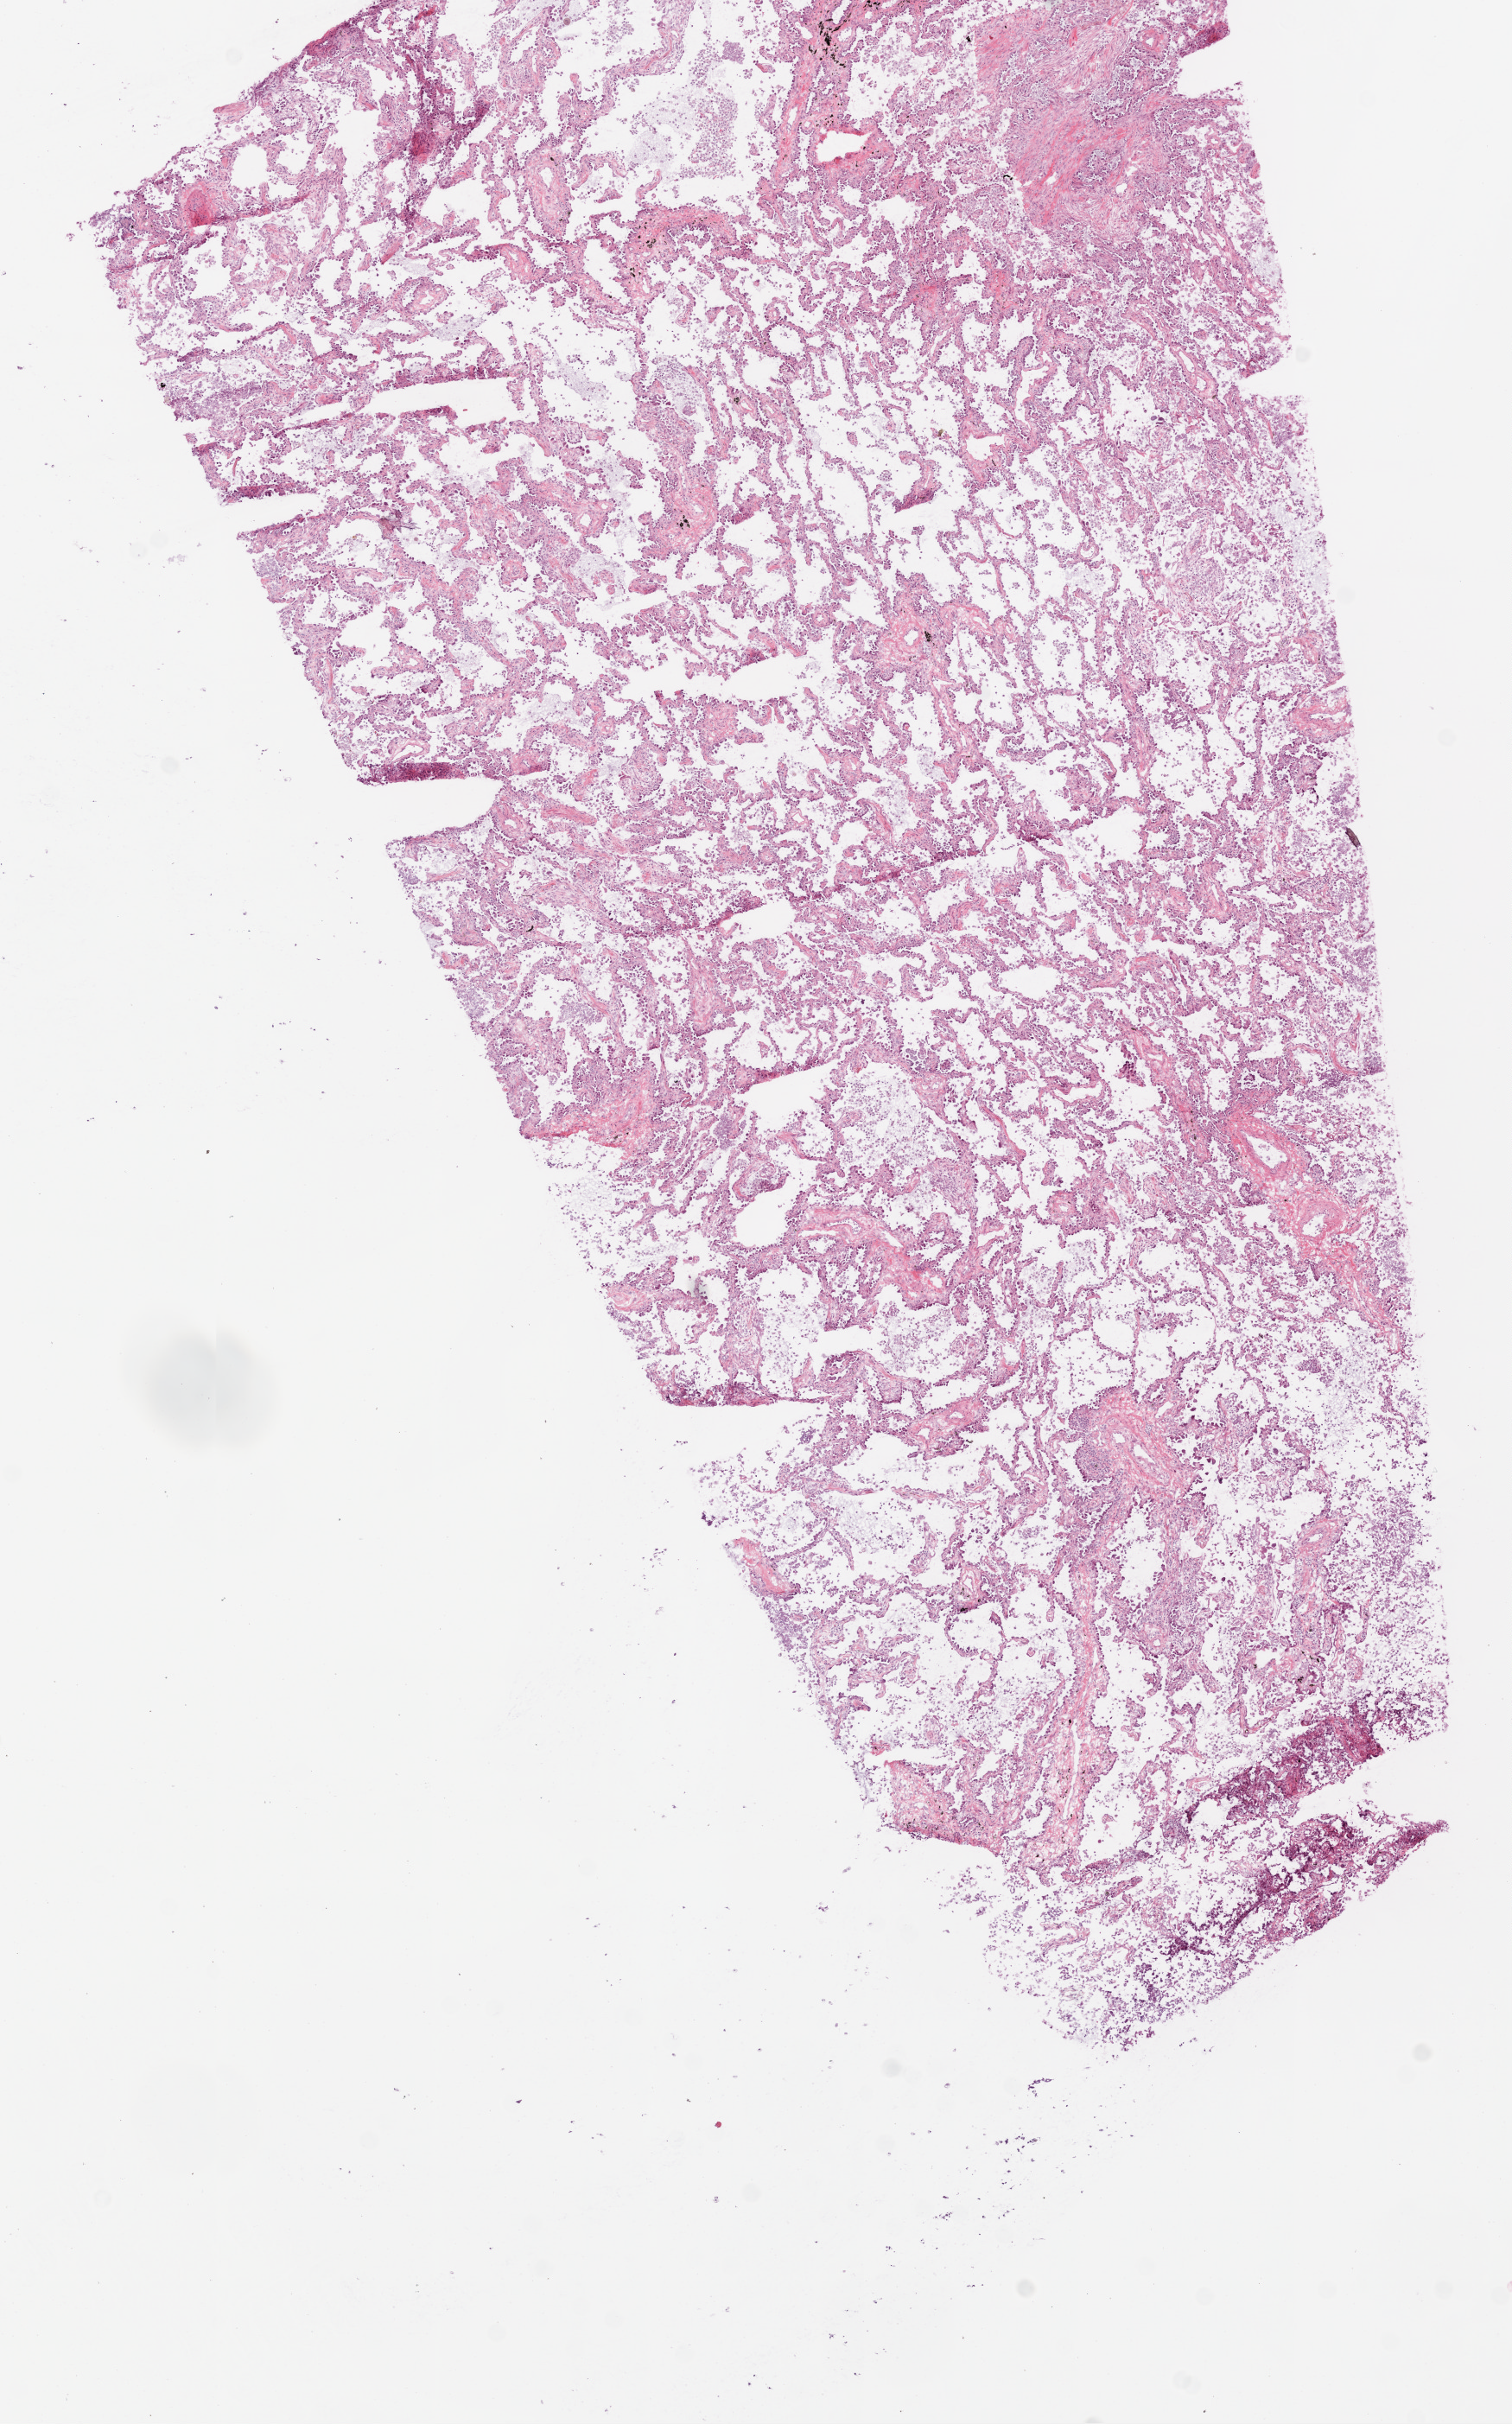
Whole-slide histology image, H&E-stained, whole scanned area (about 7.0 x 11.3 mm) shown as a low-resolution overview; frozen section from the top of the tissue portion; sample: primary tumour, lung. Female, age 57 years at initial diagnosis. Pathologist review of this section (percent, as recorded): tumour cells 95%, tumour nuclei 75%, normal cells 0%, stromal cells 5%, necrosis 0%.
Laterality: left. Diagnosis: Adenocarcinoma, NOS.